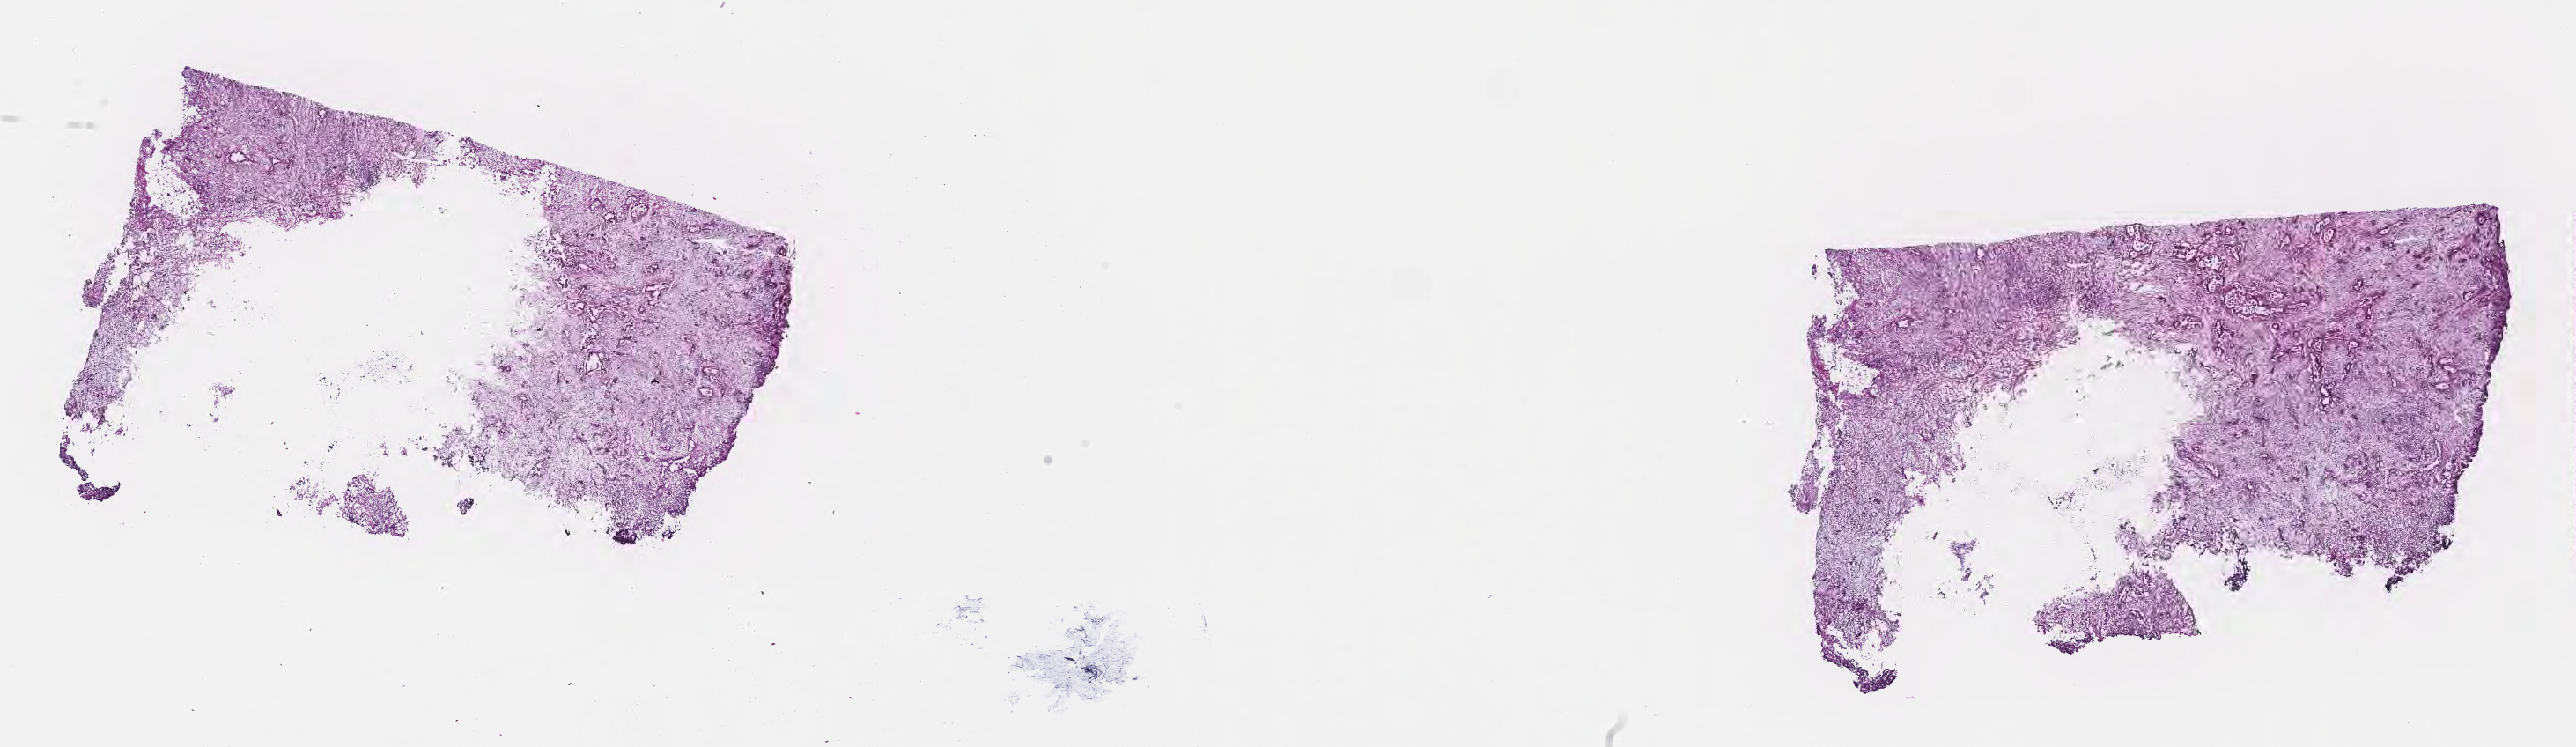
Hematoxylin and eosin (H&E) whole-slide image — a low-resolution overview of the entire scanned area, about 23.6 x 6.9 mm; frozen section (tissue freezing medium); metastatic tumor tissue, resected from lymph node. Patient: male, age at initial diagnosis 61 years. Pathologist review of this section (percent, as recorded): tumor cells 45%, tumor nuclei 45%, stromal cells 40%, necrosis 0%, normal cells 15%. Inflammatory infiltration, as recorded: lymphocyte infiltration 9%, monocyte infiltration 12%, neutrophil infiltration 9%.
Patient diagnosis (primary): Adenocarcinoma, NOS. Section: top of the tissue portion.